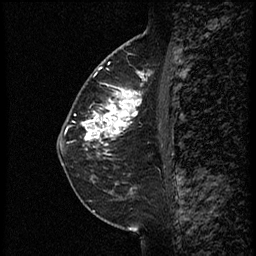
Breast MRI (dynamic contrast-enhanced), one sagittal slice. Position 30 of 60 along the scan axis. Dynamic contrast-enhanced study with each time point stored as its own series, time point 2 of 3 at this slice position (early post-contrast, ordered by acquisition time). 1.5 T. TE 4.2 ms, TR 18.9 ms. 2 mm slice thickness. 256 × 256 image matrix, field of view 200 × 200 mm. Female patient. Case-level facts recorded for this patient, not image findings: setting: breast cancer imaged before/during neoadjuvant chemotherapy; receptor status: HER2-positive.
Structures marked on this image (semi-automatic segmentation, software-assisted and operator-edited):
- analysis volume of interest (the breast-tissue region the enhancement analysis was run in; not a lesion): bounding box [x1, y1, x2, y2] px = [77, 72, 161, 147]
- tumour enhancement mask (voxels above the 100 % enhancement threshold inside the analysis volume of interest): [85, 73, 145, 147]